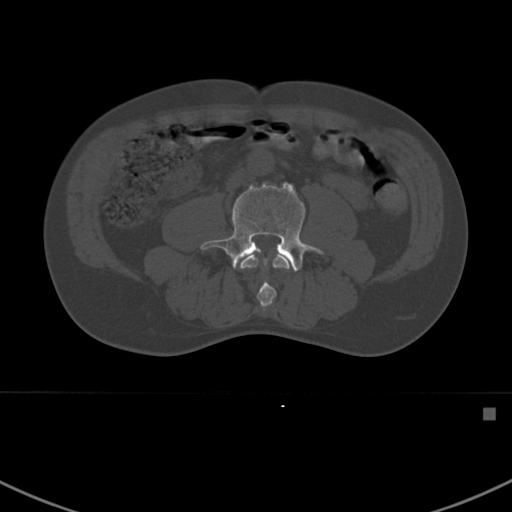
CT including the spine, one axial slice; position 248 of 412 along the scan axis; reconstruction kernel Br40s; 120 kVp; bone window (W 1800 / L 400 HU); 1.5 mm slice thickness; 512 × 512 image matrix, field of view 358 × 358 mm. Patient: male, 59 years. Case-level facts recorded for this patient, not image findings: primary cancer: prostate.
Structures marked on this image (semi-automatically segmented with operator editing):
- L3 vertebra: box from (x=239, y=254) to (x=294, y=312) px
- L4 vertebra: (x=200, y=182)–(x=324, y=271)